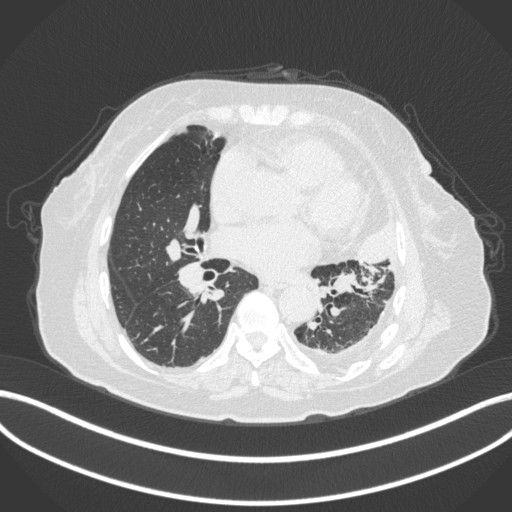
Chest CT, one axial slice; slice 174 of 399 in the series (ordered by position); 120 kVp; lung window (W 1500 / L -600 HU); 1 mm slice thickness; 512 × 512 image matrix, field of view 400 × 400 mm. Female patient, age 75 years. From the clinical record (not read from this slice): clinical TNM (as recorded): T3 N3 M1.
Annotated regions visible in this slice (rectangle marked by the reading radiologist):
- lung tumour (recorded histology: adenocarcinoma): bounding box (x1, y1, x2, y2) in pixels: (356, 222, 397, 271)